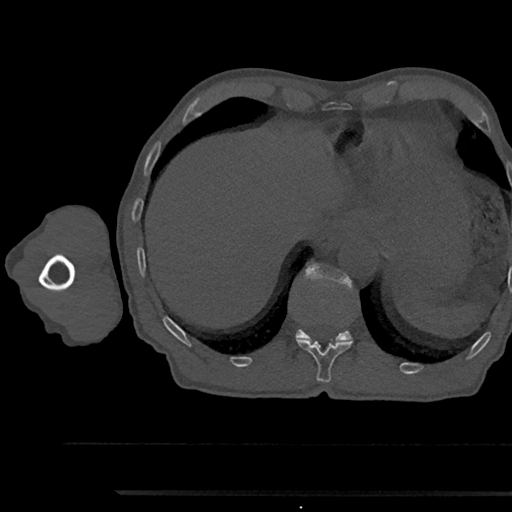
CT including the spine, one axial slice. Position 758 of 797 along the scan axis. Bone window (W 1800 / L 400 HU). 512 × 512 image matrix, field of view 367 × 367 mm. Male patient, age 79 years. Case-level facts recorded for this patient, not image findings: primary cancer: prostate.
Outlined on this slice (semi-automatically segmented with operator editing):
- T11 vertebra: bounding box (x1, y1, x2, y2) in pixels: (297, 338, 352, 383)
- T12 vertebra: (295, 264, 355, 342)